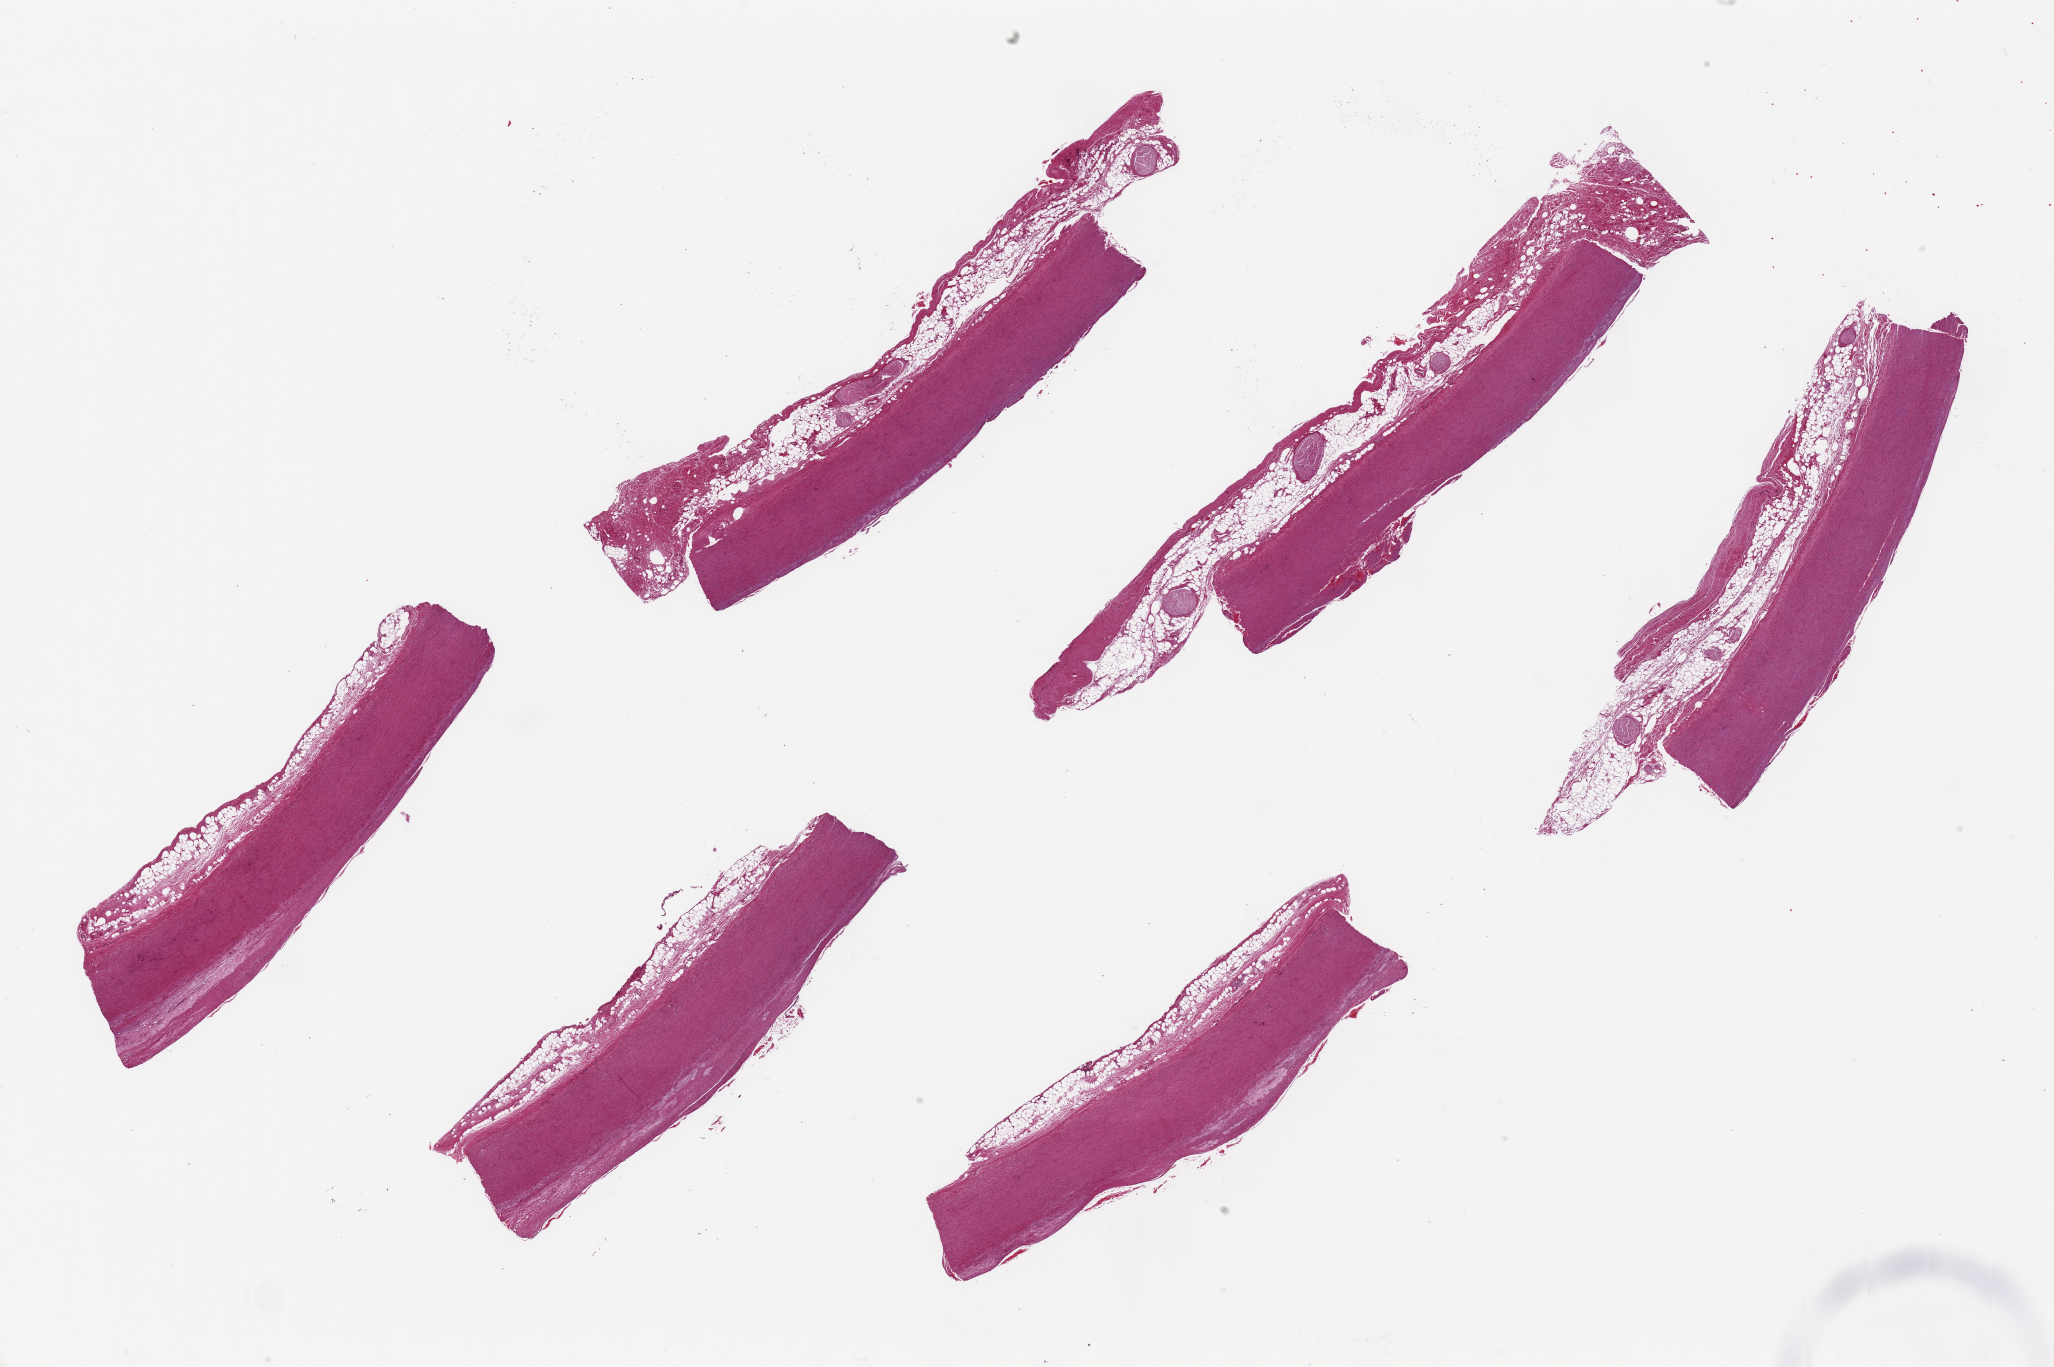
Digitized haematoxylin and eosin-stained section, brightfield, shown as a low-resolution overview of the whole scanned area (about 32.5 x 21.6 mm), PAXgene-fixed paraffin-embedded (PFPE) section, sampled site (target tissue): aorta, donor tissue sample. Donor sex: female.
Reviewer comment on this tissue sample: 6 pieces, 8x1.5mm, NOTE :all have 0.5`1mm layer of adherent fibroadipose tissue.